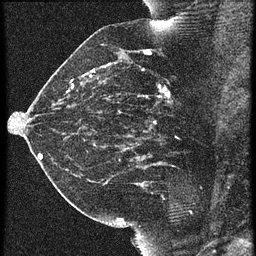
Breast MRI (dynamic contrast-enhanced), one sagittal slice. 3 images stored at this slice position (order not interpretable as contrast timing). 1.5 T. TE 4.2 ms, TR 21.3 ms. 1.5 mm slice thickness. 256 × 256 image matrix, field of view 180 × 180 mm. Female patient, age 42 years. From the clinical record (not read from this slice): setting: breast cancer imaged before/during neoadjuvant chemotherapy; receptor status: HER2-positive.
Annotated regions visible in this slice (semi-automatically segmented with operator editing):
- analysis volume of interest (the breast-tissue region the enhancement analysis was run in; not a lesion): bounding box (x1, y1, x2, y2) in pixels: (122, 82, 195, 147)
- tumour enhancement mask (voxels above the 90 % enhancement threshold inside the analysis volume of interest): (145, 86, 171, 99)